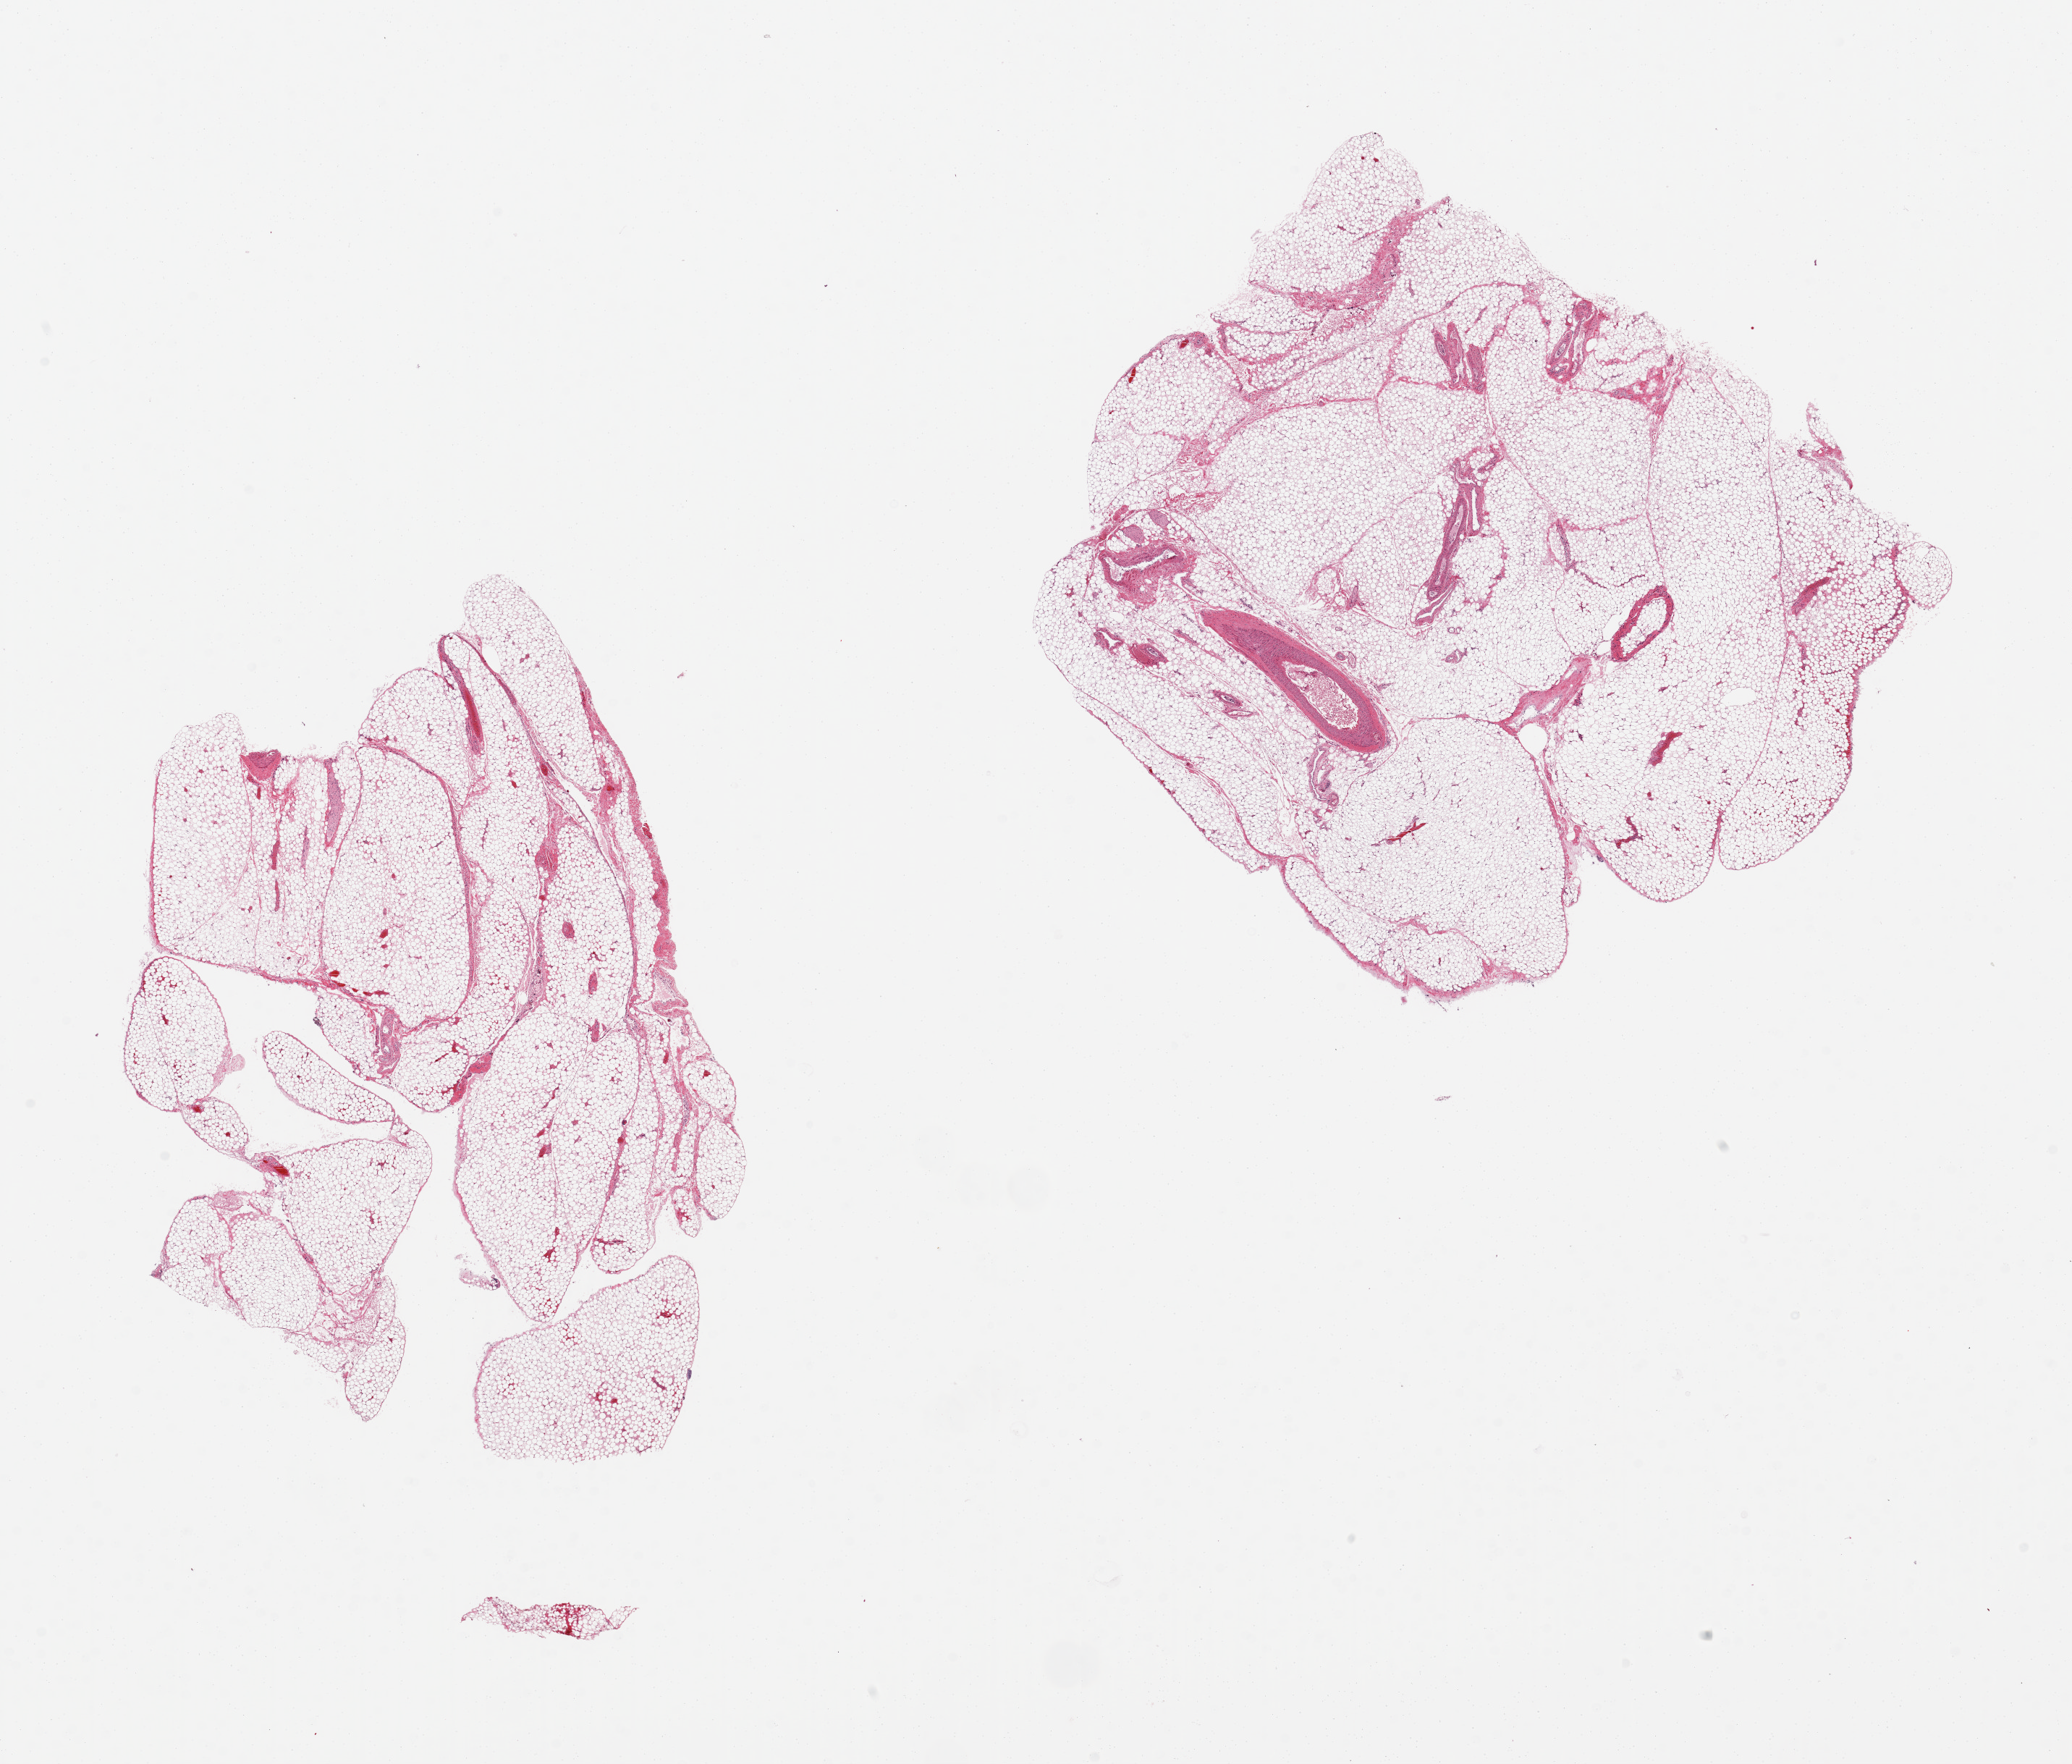
Digitized H&E-stained section, whole scanned area (about 22.6 x 19.3 mm, acquisition: 20x scan) shown as a low-resolution overview; PAXgene-fixed paraffin-embedded (PFPE) section; section of omentum (target tissue); tissue donor sample. Donor: male.
Review note (as recorded): 2 pieces.